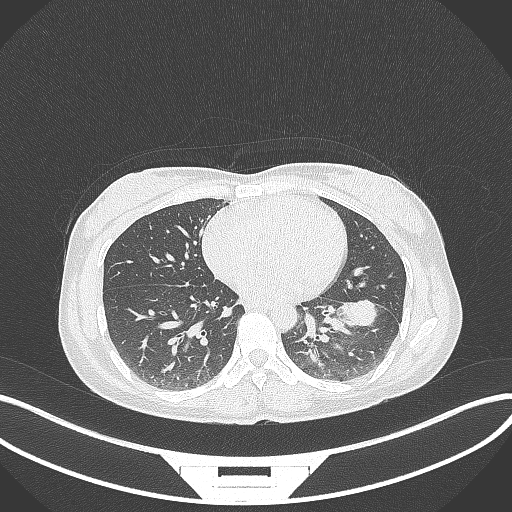
Chest CT, one axial slice. Slice 31 of 244 in the series (ordered by position). 120 kVp. Lung window (W 1500 / L -600 HU). 1 mm slice thickness. 512 × 512 image matrix, field of view 400 × 400 mm. Patient: female, 41 years. Case-level facts recorded for this patient, not image findings: clinical TNM (as recorded): T2a N3 M1b.
Annotated regions visible in this slice (bounding box drawn by a radiologist):
- lung tumour (recorded histology: adenocarcinoma): bounding box [x1, y1, x2, y2] px = [333, 299, 385, 331]